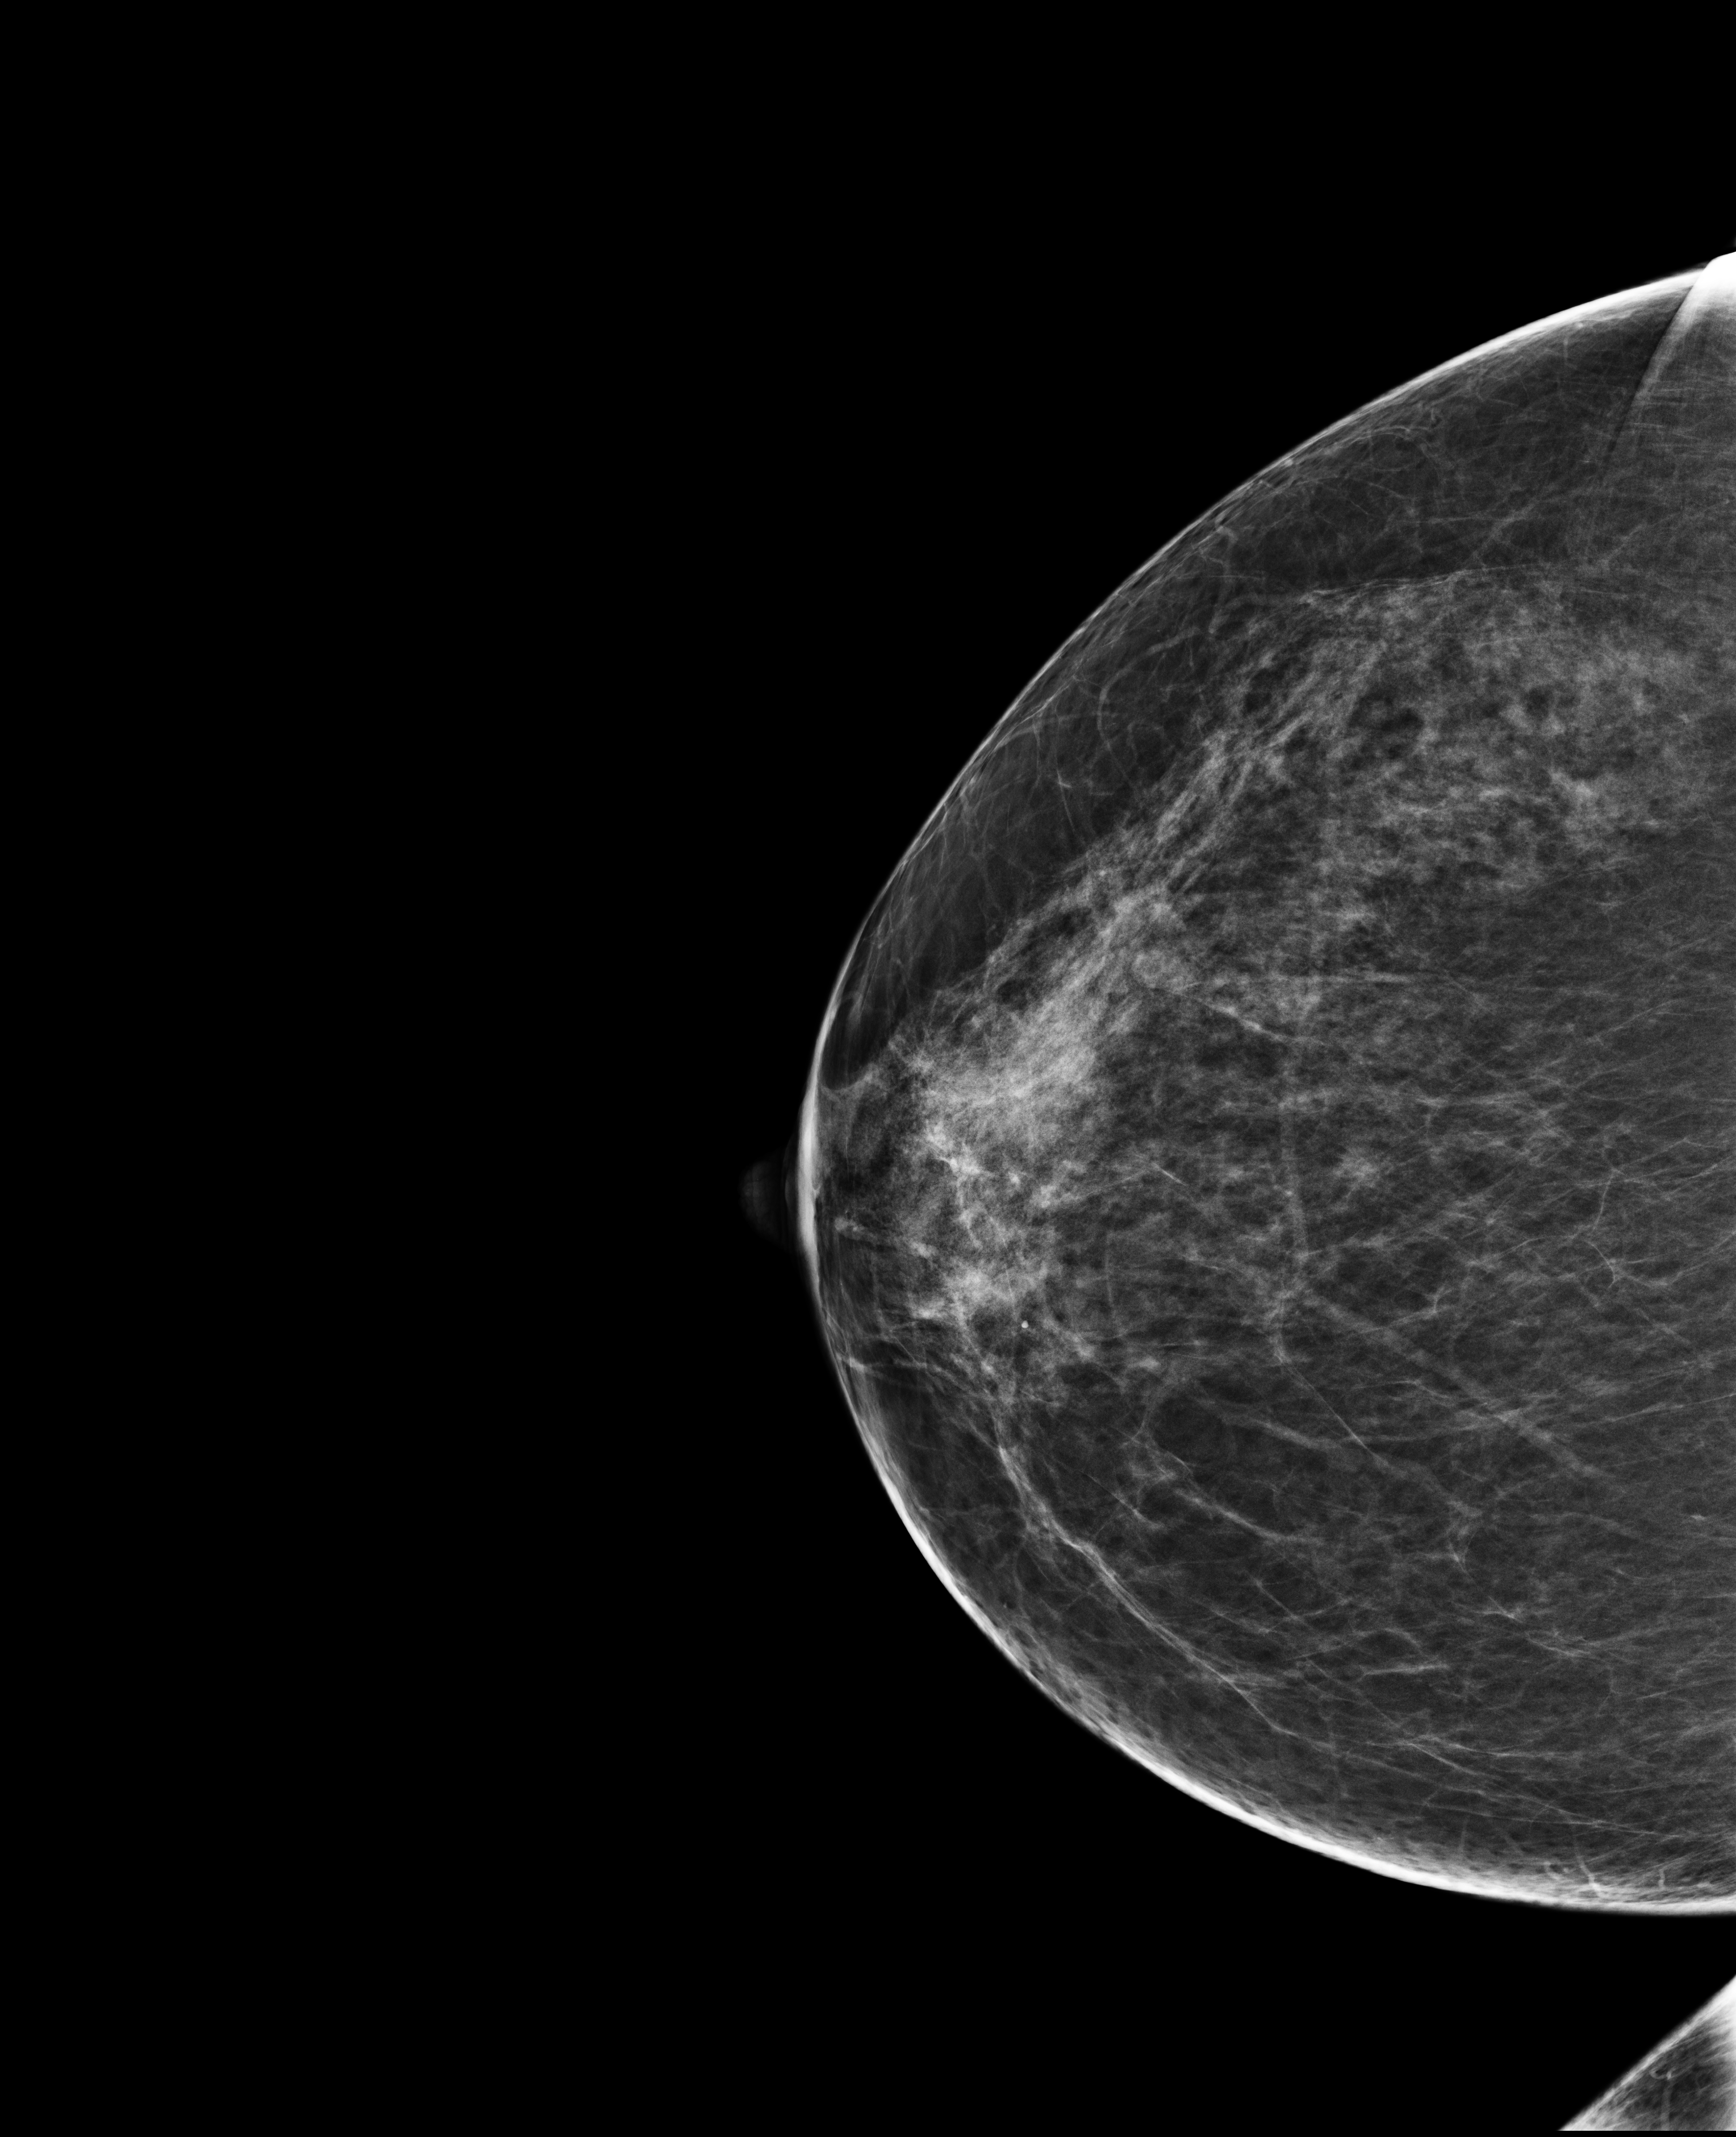
Digital mammogram (FFDM); right breast; craniocaudal (CC) view; screening examination; system: Selenia Dimensions. Patient aged 47 years (female).
- BI-RADS breast density category at the screening exam (both breasts, scale 1–4): 3
- final BI-RADS assessment for this screening round (tomosynthesis exam, both breasts): category 4
- recall: recalled for additional imaging after this screen